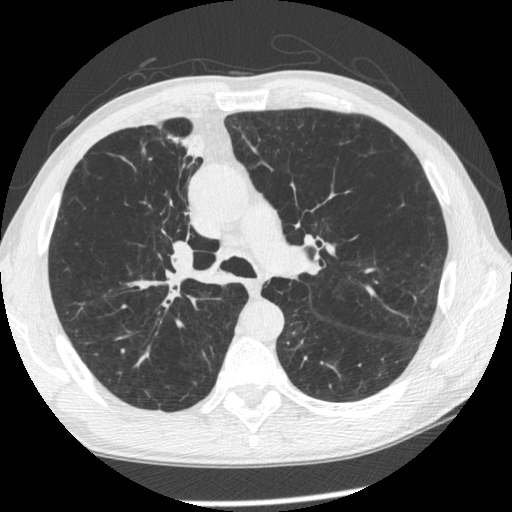
Low-dose screening chest CT, one axial slice. Reconstruction kernel STANDARD. 120 kVp. Lung window (W 1500 / L -600 HU). 512 × 512 image matrix.
Annotated regions visible in this slice (expert manual segmentation):
- lesion 1 (tumor, upper lobe of right lung): bounding box <181,134,204,158> (left, top, right, bottom; pixels)